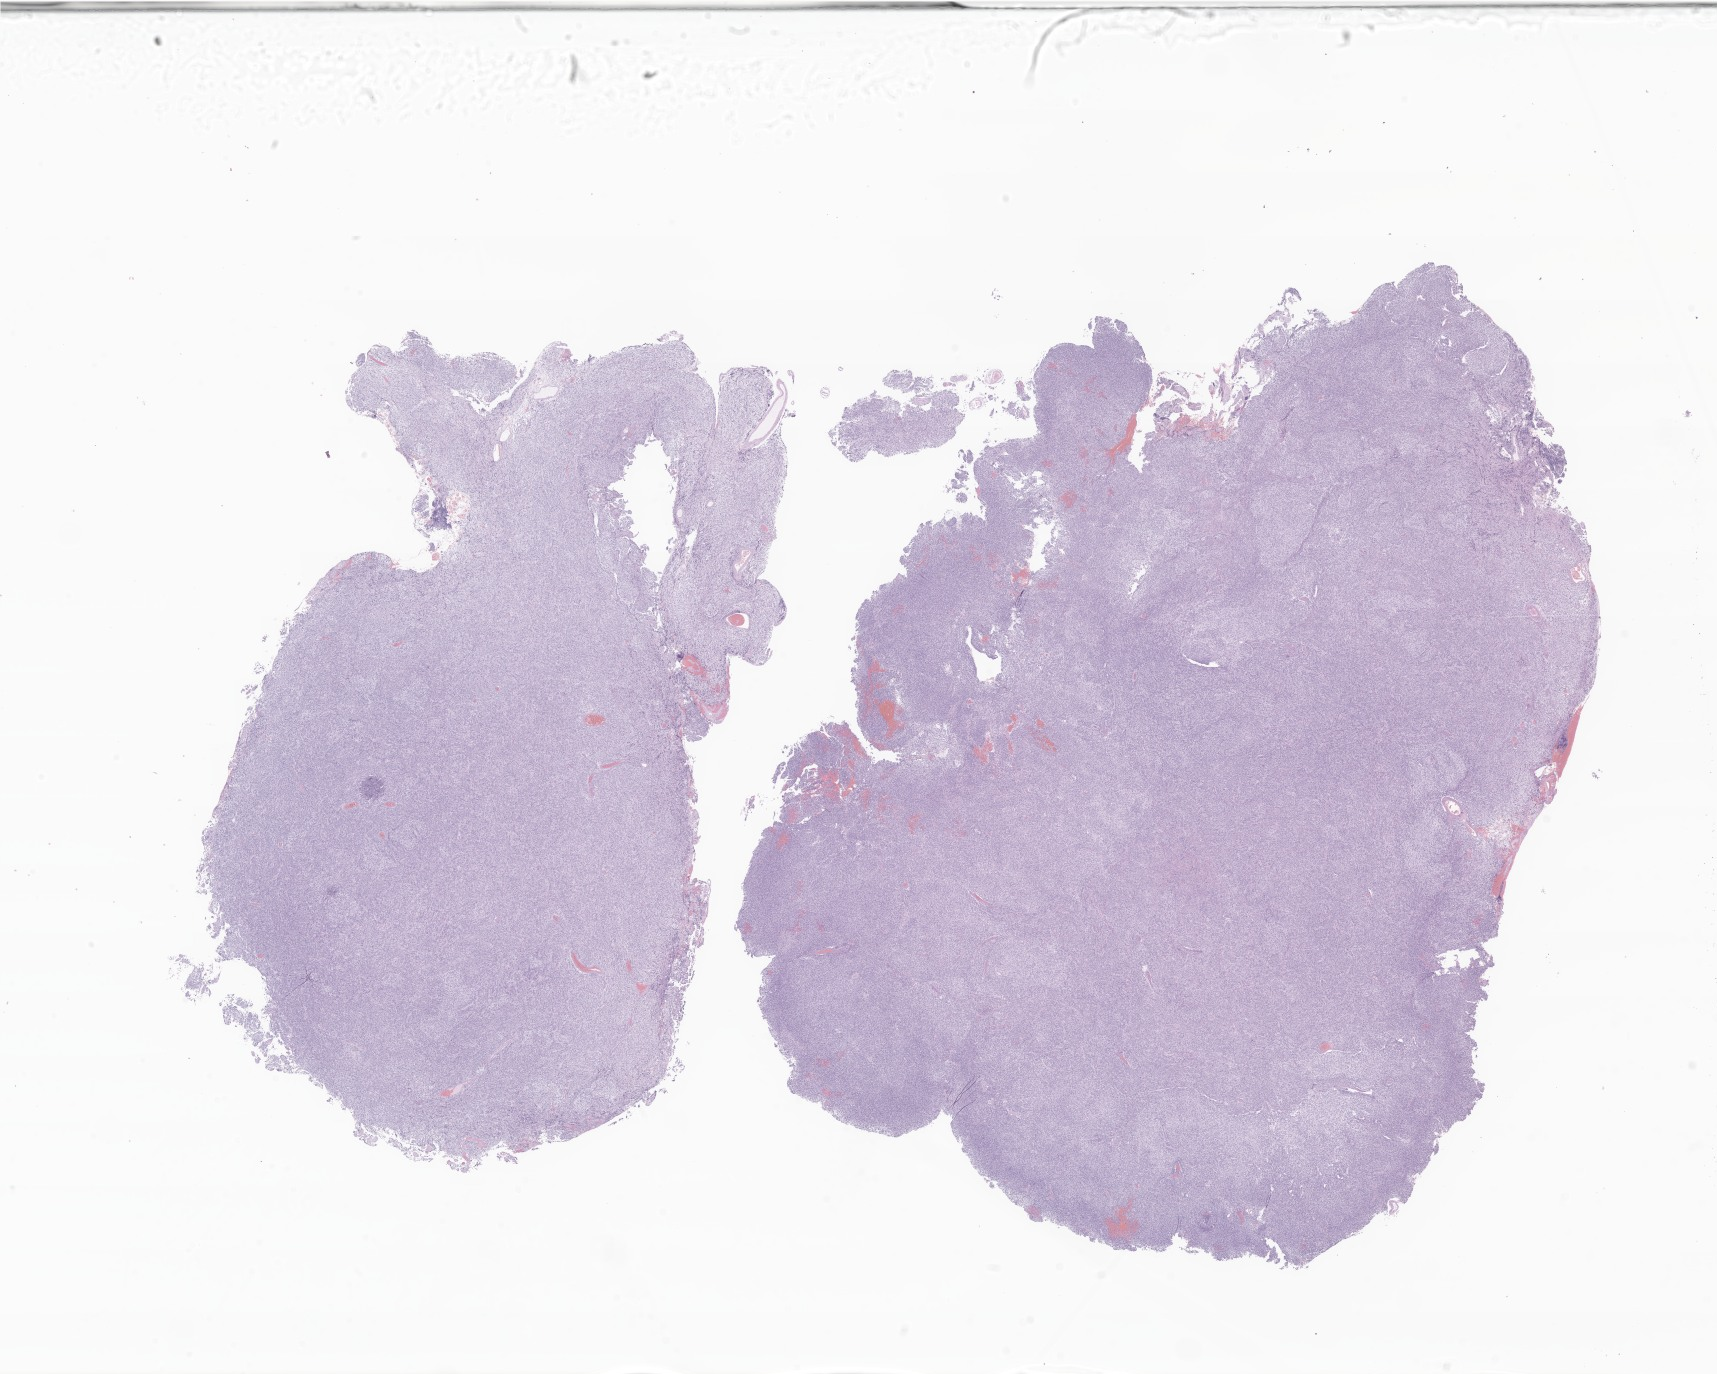
Digitized haematoxylin and eosin-stained section of tumor tissue from the cerebral ventricle — low-resolution overview of the scanned area, about 29.0 x 23.2 mm; FFPE section. Patient: male, age 102 months.
- diagnosis (ICD-O-3 morphology term): Medulloblastoma, NOS